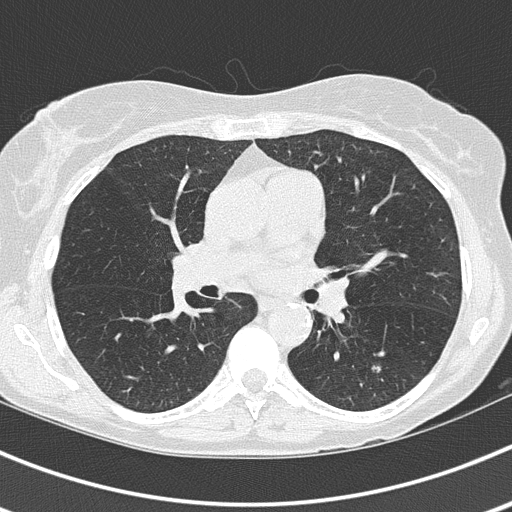
Low-dose screening chest CT, axial slice. Baseline annual screen. Lung window (W 1500 / L -600 HU). Lung (sharp) reconstruction kernel (B50f). Slice 69 of 143 in the series. 512 × 512 image matrix, field of view 310 × 310 mm. Female, age 60 years at enrolment.
• Expert-annotated lung lesion, bounding box [x1, y1, x2, y2] px = [359, 352, 391, 382].
• No non-calcified nodule or mass ≥4 mm was recorded by the screening reader at this exam.
• Official screen result: negative screen, no significant abnormalities.
• Participant outcome: lung cancer diagnosed 403 days after this screen — adenocarcinoma, NOS, left lower lobe, well differentiated (G1), stage IA (AJCC 6th edition), 15 mm at pathology.